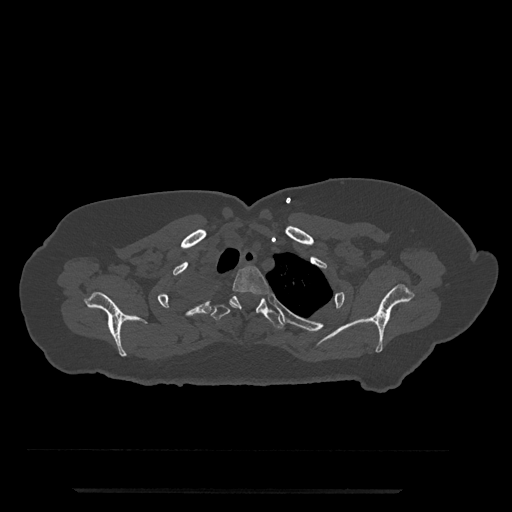
CT including the spine, one axial slice; slice 653 of 797 in the series (ordered by position); 120 kVp; bone window (W 1800 / L 400 HU); 512 × 512 image matrix, field of view 440 × 440 mm. Female patient, age 51 years. Case-level facts recorded for this patient, not image findings: primary cancer: neuro.
Structures marked on this image (semi-automatic segmentation, software-assisted and operator-edited):
- T2 vertebra: bounding box (x1, y1, x2, y2) in pixels: (230, 266, 269, 306)
- T3 vertebra: (210, 296, 284, 329)